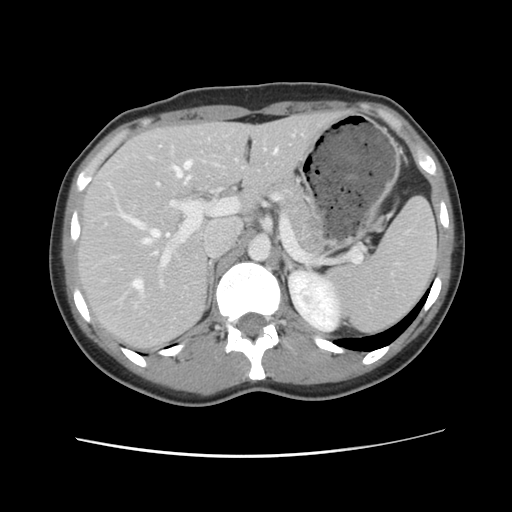
Contrast-enhanced abdominal CT, one axial slice; slice 69 of 134 in the series (ordered by position); intravenous contrast given; soft-tissue window (W 400 / L 40 HU); 2.5 mm slice thickness; 512 × 512 image matrix, field of view 339 × 339 mm. Female patient, age 33 years. Case-level facts recorded for this patient, not image findings: diagnosis: colorectal cancer liver metastases, imaged before liver resection; multiple liver metastases: yes; largest metastasis: 4.5 cm; chemotherapy before resection: no.
Annotated regions visible in this slice (outlined manually by an expert reader):
- hepatic veins: box from (x=126, y=149) to (x=279, y=298) px
- liver: (x=79, y=113)–(x=339, y=351)
- planned liver remnant (the part of the liver to remain after resection): (x=79, y=113)–(x=339, y=351)
- portal vein (with intrahepatic branches): (x=151, y=139)–(x=267, y=288)